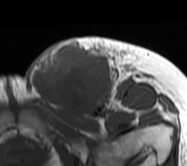
MRI of an extremity soft-tissue mass, one axial slice. Position 32 of 62 along the scan axis. MR volume resampled by the dataset authors to the PET/CT grid (not the native acquisition matrix). 3.27 mm slice thickness. 187 × 166 image matrix, field of view 183 × 162 mm. Female patient. Case-level facts recorded for this patient, not image findings: histological type: leiomyosarcoma; grade: high; site of the primary tumour: groin.
Annotated regions visible in this slice (expert contour drawn on MRI and transferred to this co-registered scan by the dataset authors):
- gross tumour volume including surrounding oedema: bounding box <27,37,142,118> (left, top, right, bottom; pixels)
- gross tumour volume (mass): <27,42,115,116>